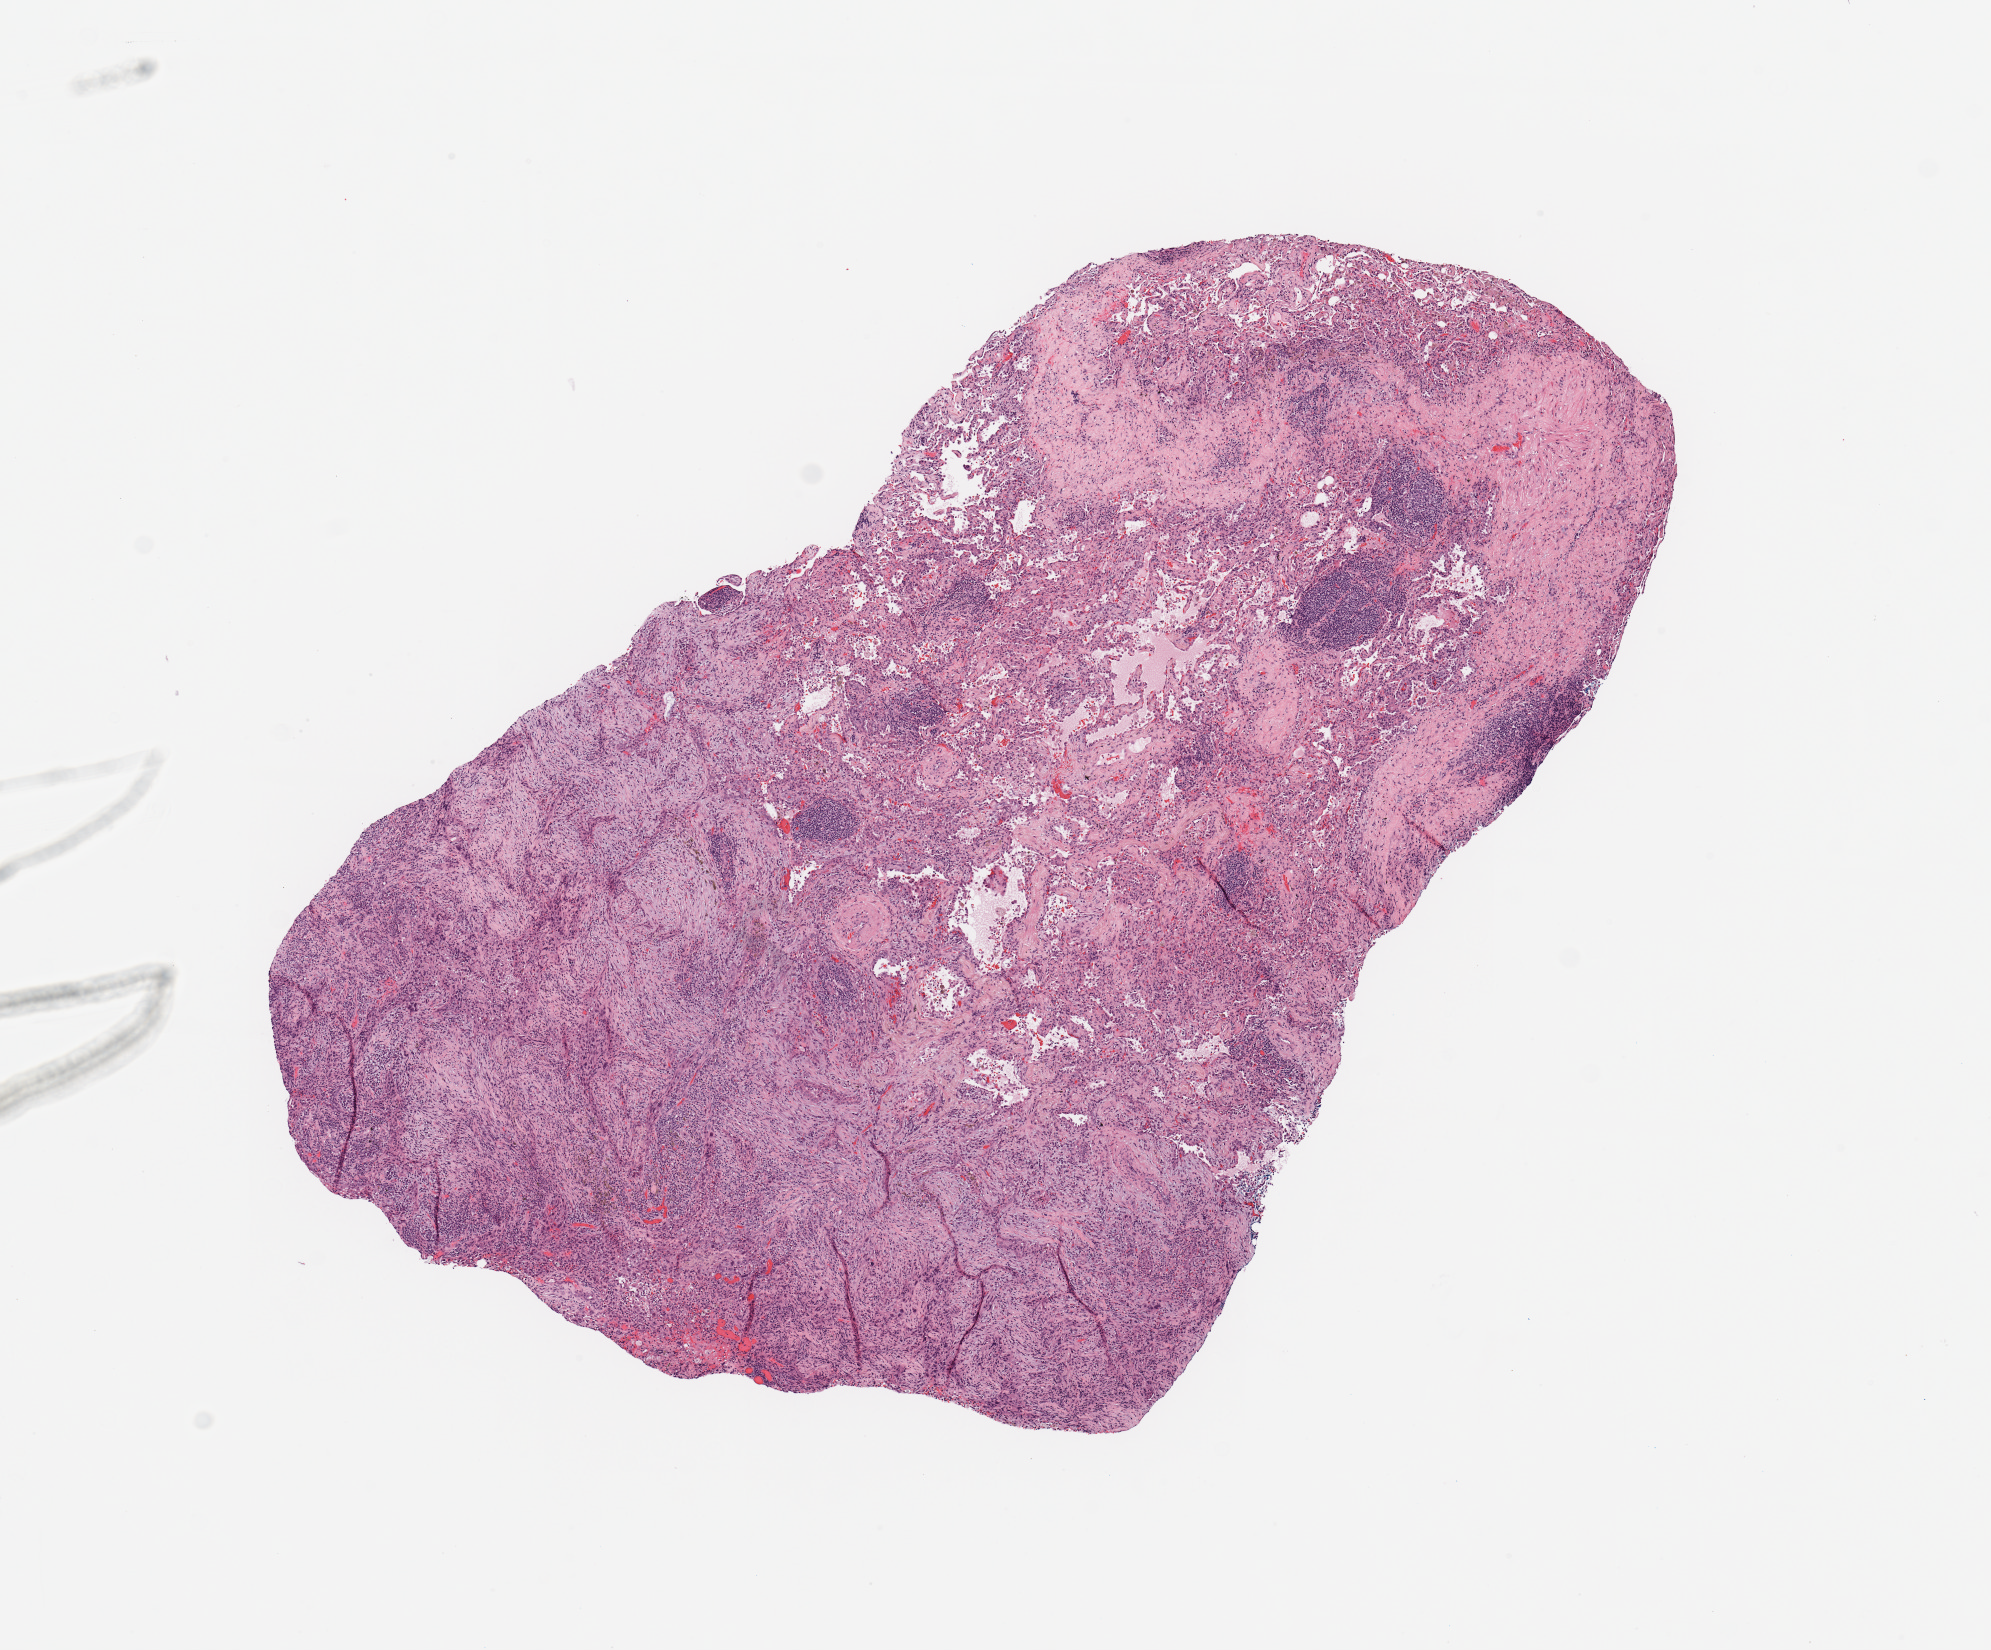
Whole-slide histology image, H&E, shown as a low-resolution overview of the whole scanned area (about 7.9 x 6.5 mm, acquisition: 20x scan), tumour tissue sample, lung. 69-year-old male patient. Histologic grade: G3 (poorly differentiated).
* diagnosis: Squamous cell carcinoma, NOS
* primary tumour site (as recorded): right upper lobe
* AJCC pathologic stage: IB